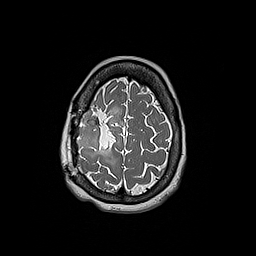
Brain MRI from a brain-tumour surgery series, one axial slice. Slice 50 of 192 in the series (ordered by position). 1 mm slice thickness. 256 × 256 image matrix, field of view 250 × 250 mm. From the clinical record (not read from this slice): histopathology: Oligodendroglioma; WHO grade: 3; IDH mutation: yes; tumour location: Right Frontal.
Structures marked on this image (manually delineated by an expert):
- tumour: bounding box <76,111,102,153> (left, top, right, bottom; pixels)